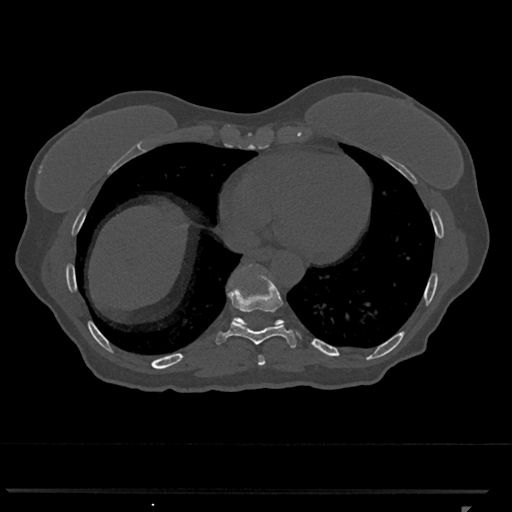
CT including the spine, one axial slice. Slice 611 of 793 in the series (ordered by position). Bone window (W 1800 / L 400 HU). 0.5 mm slice thickness. 512 × 512 image matrix, field of view 380 × 380 mm. Patient: female, 62 years. Case-level facts recorded for this patient, not image findings: primary cancer: renal.
Annotated regions visible in this slice (semi-automatic segmentation, software-assisted and operator-edited):
- T10 vertebra: box from (x=233, y=265) to (x=284, y=326) px
- T8 vertebra: (x=258, y=355)–(x=265, y=366)
- T9 vertebra: (x=216, y=275)–(x=297, y=348)